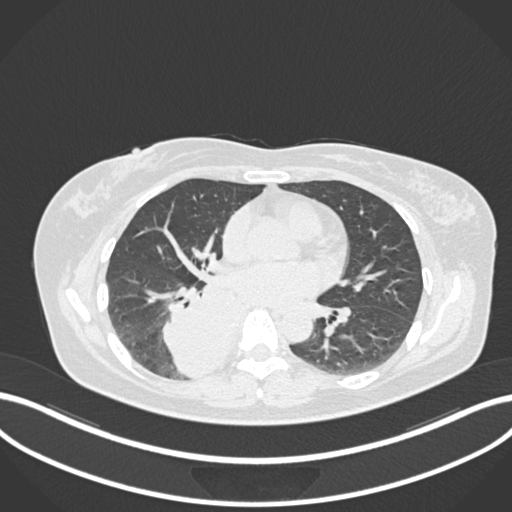
Chest CT, one axial slice. Position 581 of 677 along the scan axis. Lung window (W 1500 / L -600 HU). 1 mm slice thickness. 512 × 512 image matrix, field of view 400 × 400 mm. Female patient, age 54 years. From the clinical record (not read from this slice): clinical TNM (as recorded): T4 N0 M0.
Structures marked on this image (rectangle marked by the reading radiologist):
- lung tumour (recorded histology: adenocarcinoma): bounding box (x1, y1, x2, y2) in pixels: (155, 282, 245, 379)